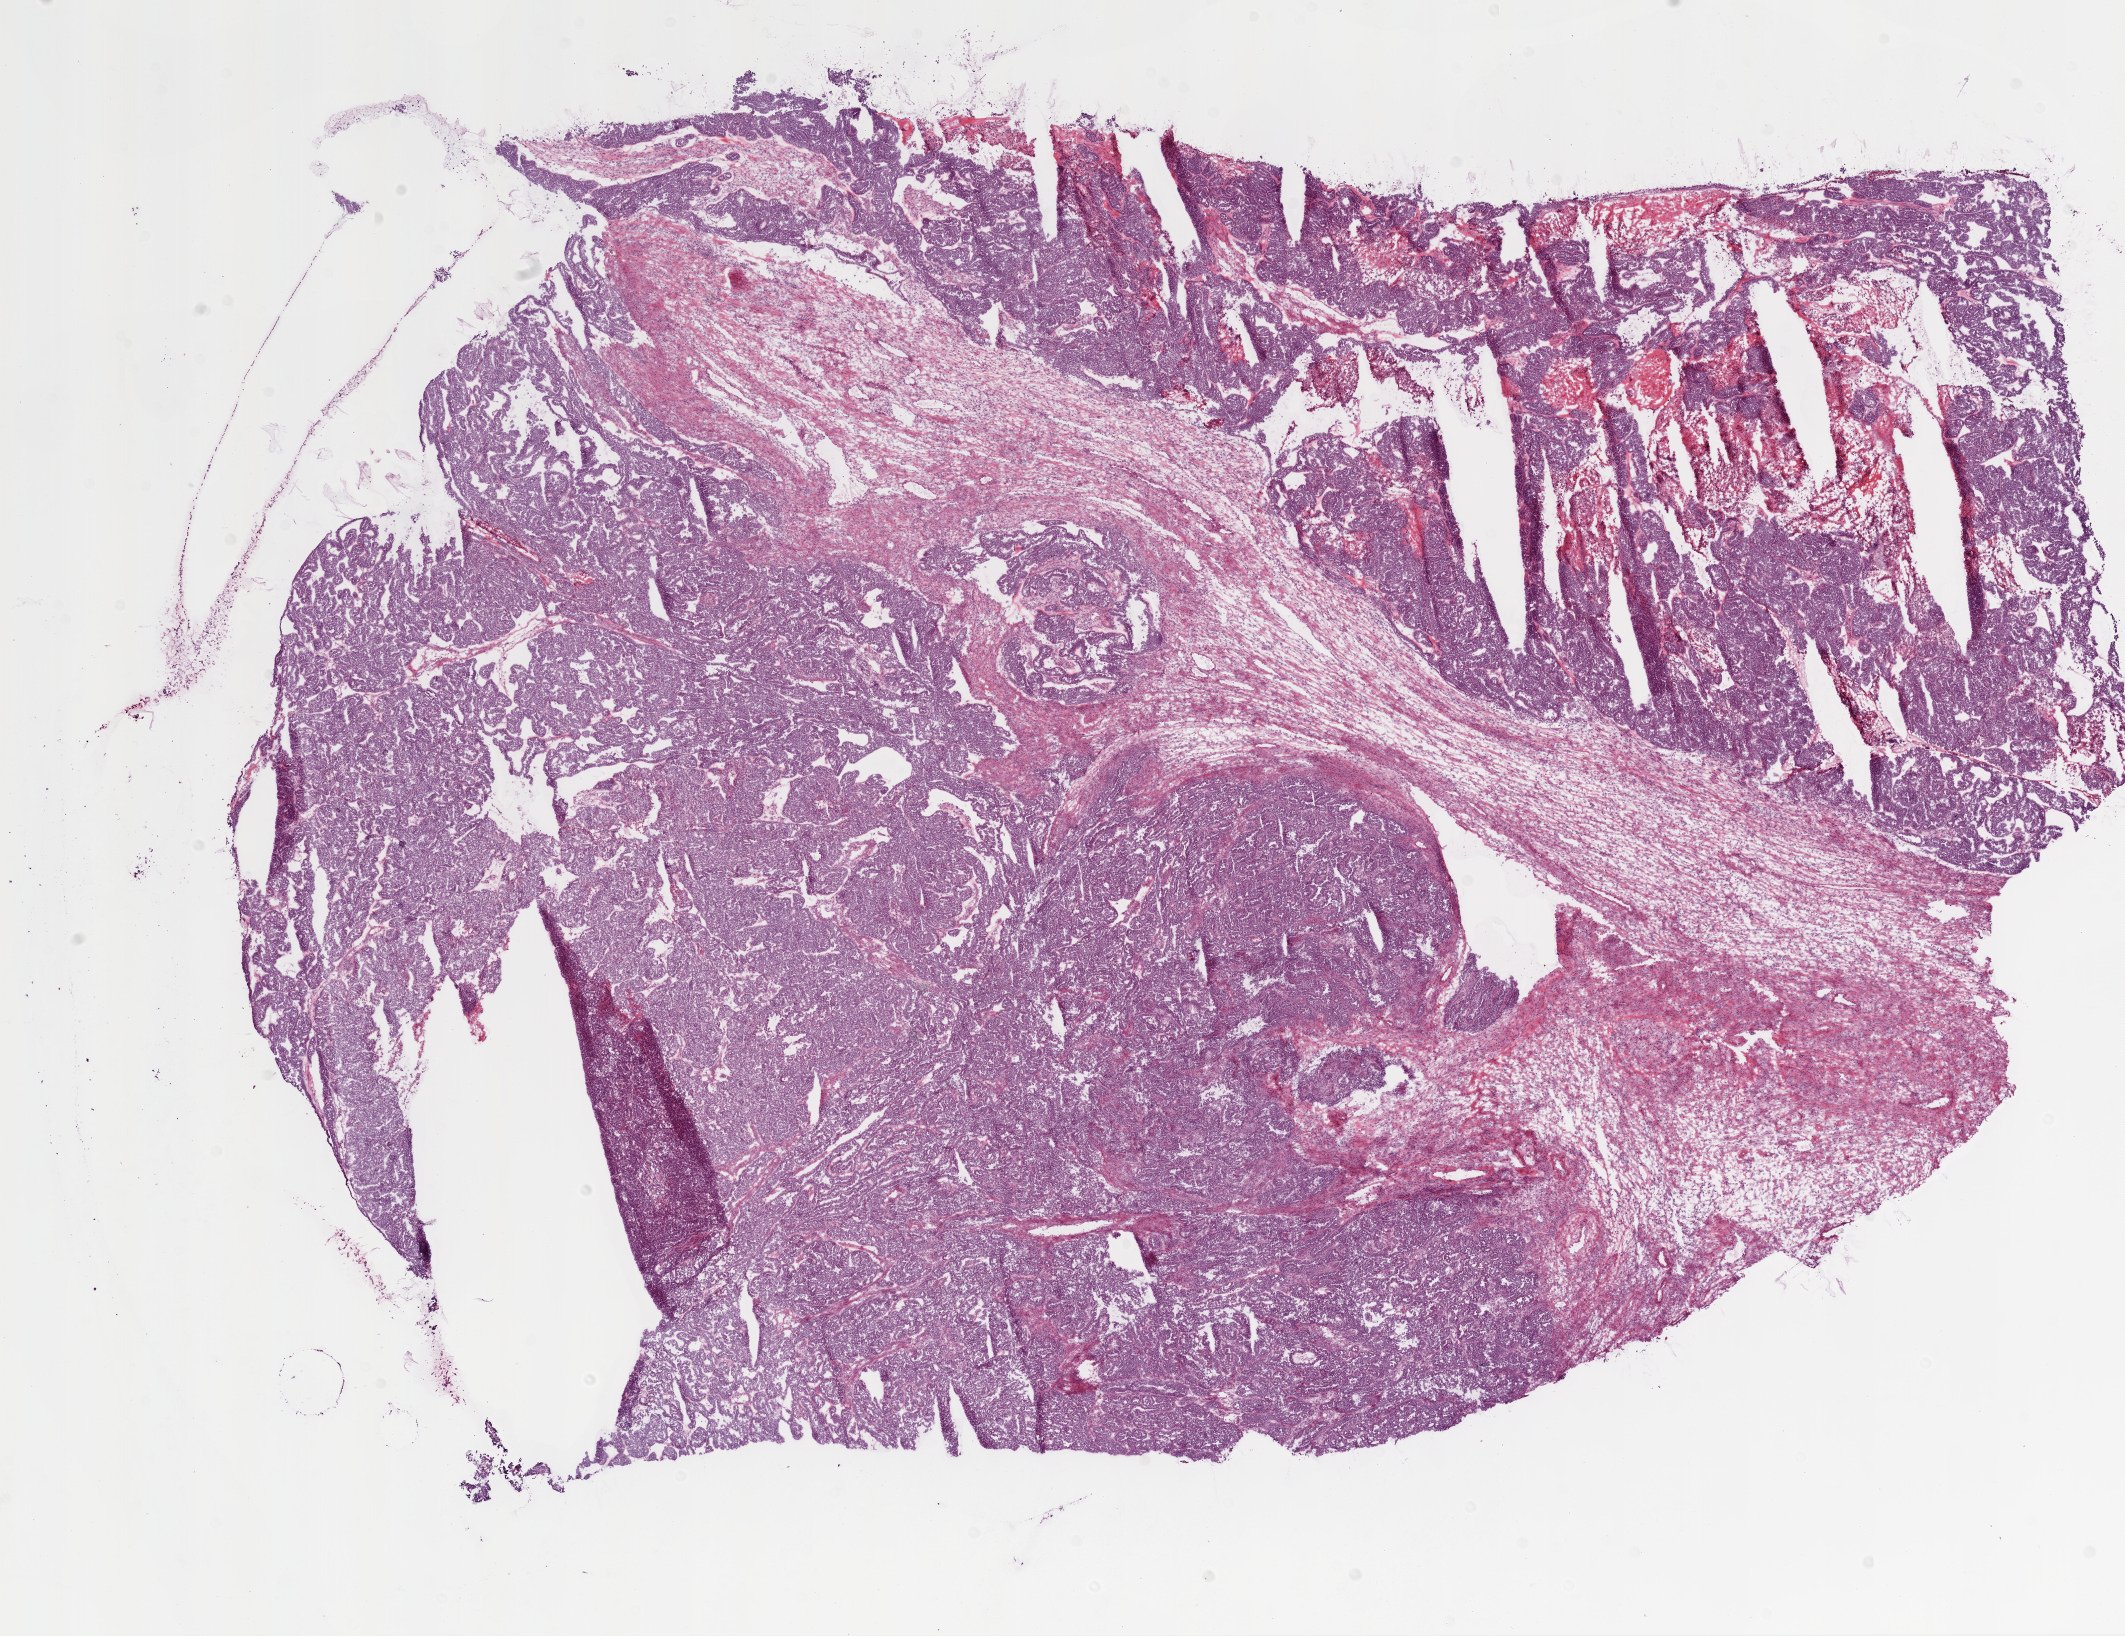
Digitized H&E tissue section (whole slide) — shown as a low-resolution overview of the whole scanned area (about 17.1 x 13.1 mm). Frozen section from the bottom of the tissue portion. Ovary, primary tumour sample. Patient: female, age at initial diagnosis 51 years. Histologic grade: G3 (poorly differentiated). Pathologist review of this section (percent, as recorded): tumour cells 80%, tumour nuclei 90%, normal cells 0%, stromal cells 10%, necrosis 10%.
FIGO stage: IIIB. Laterality: bilateral. Histologic diagnosis: Serous cystadenocarcinoma, NOS.